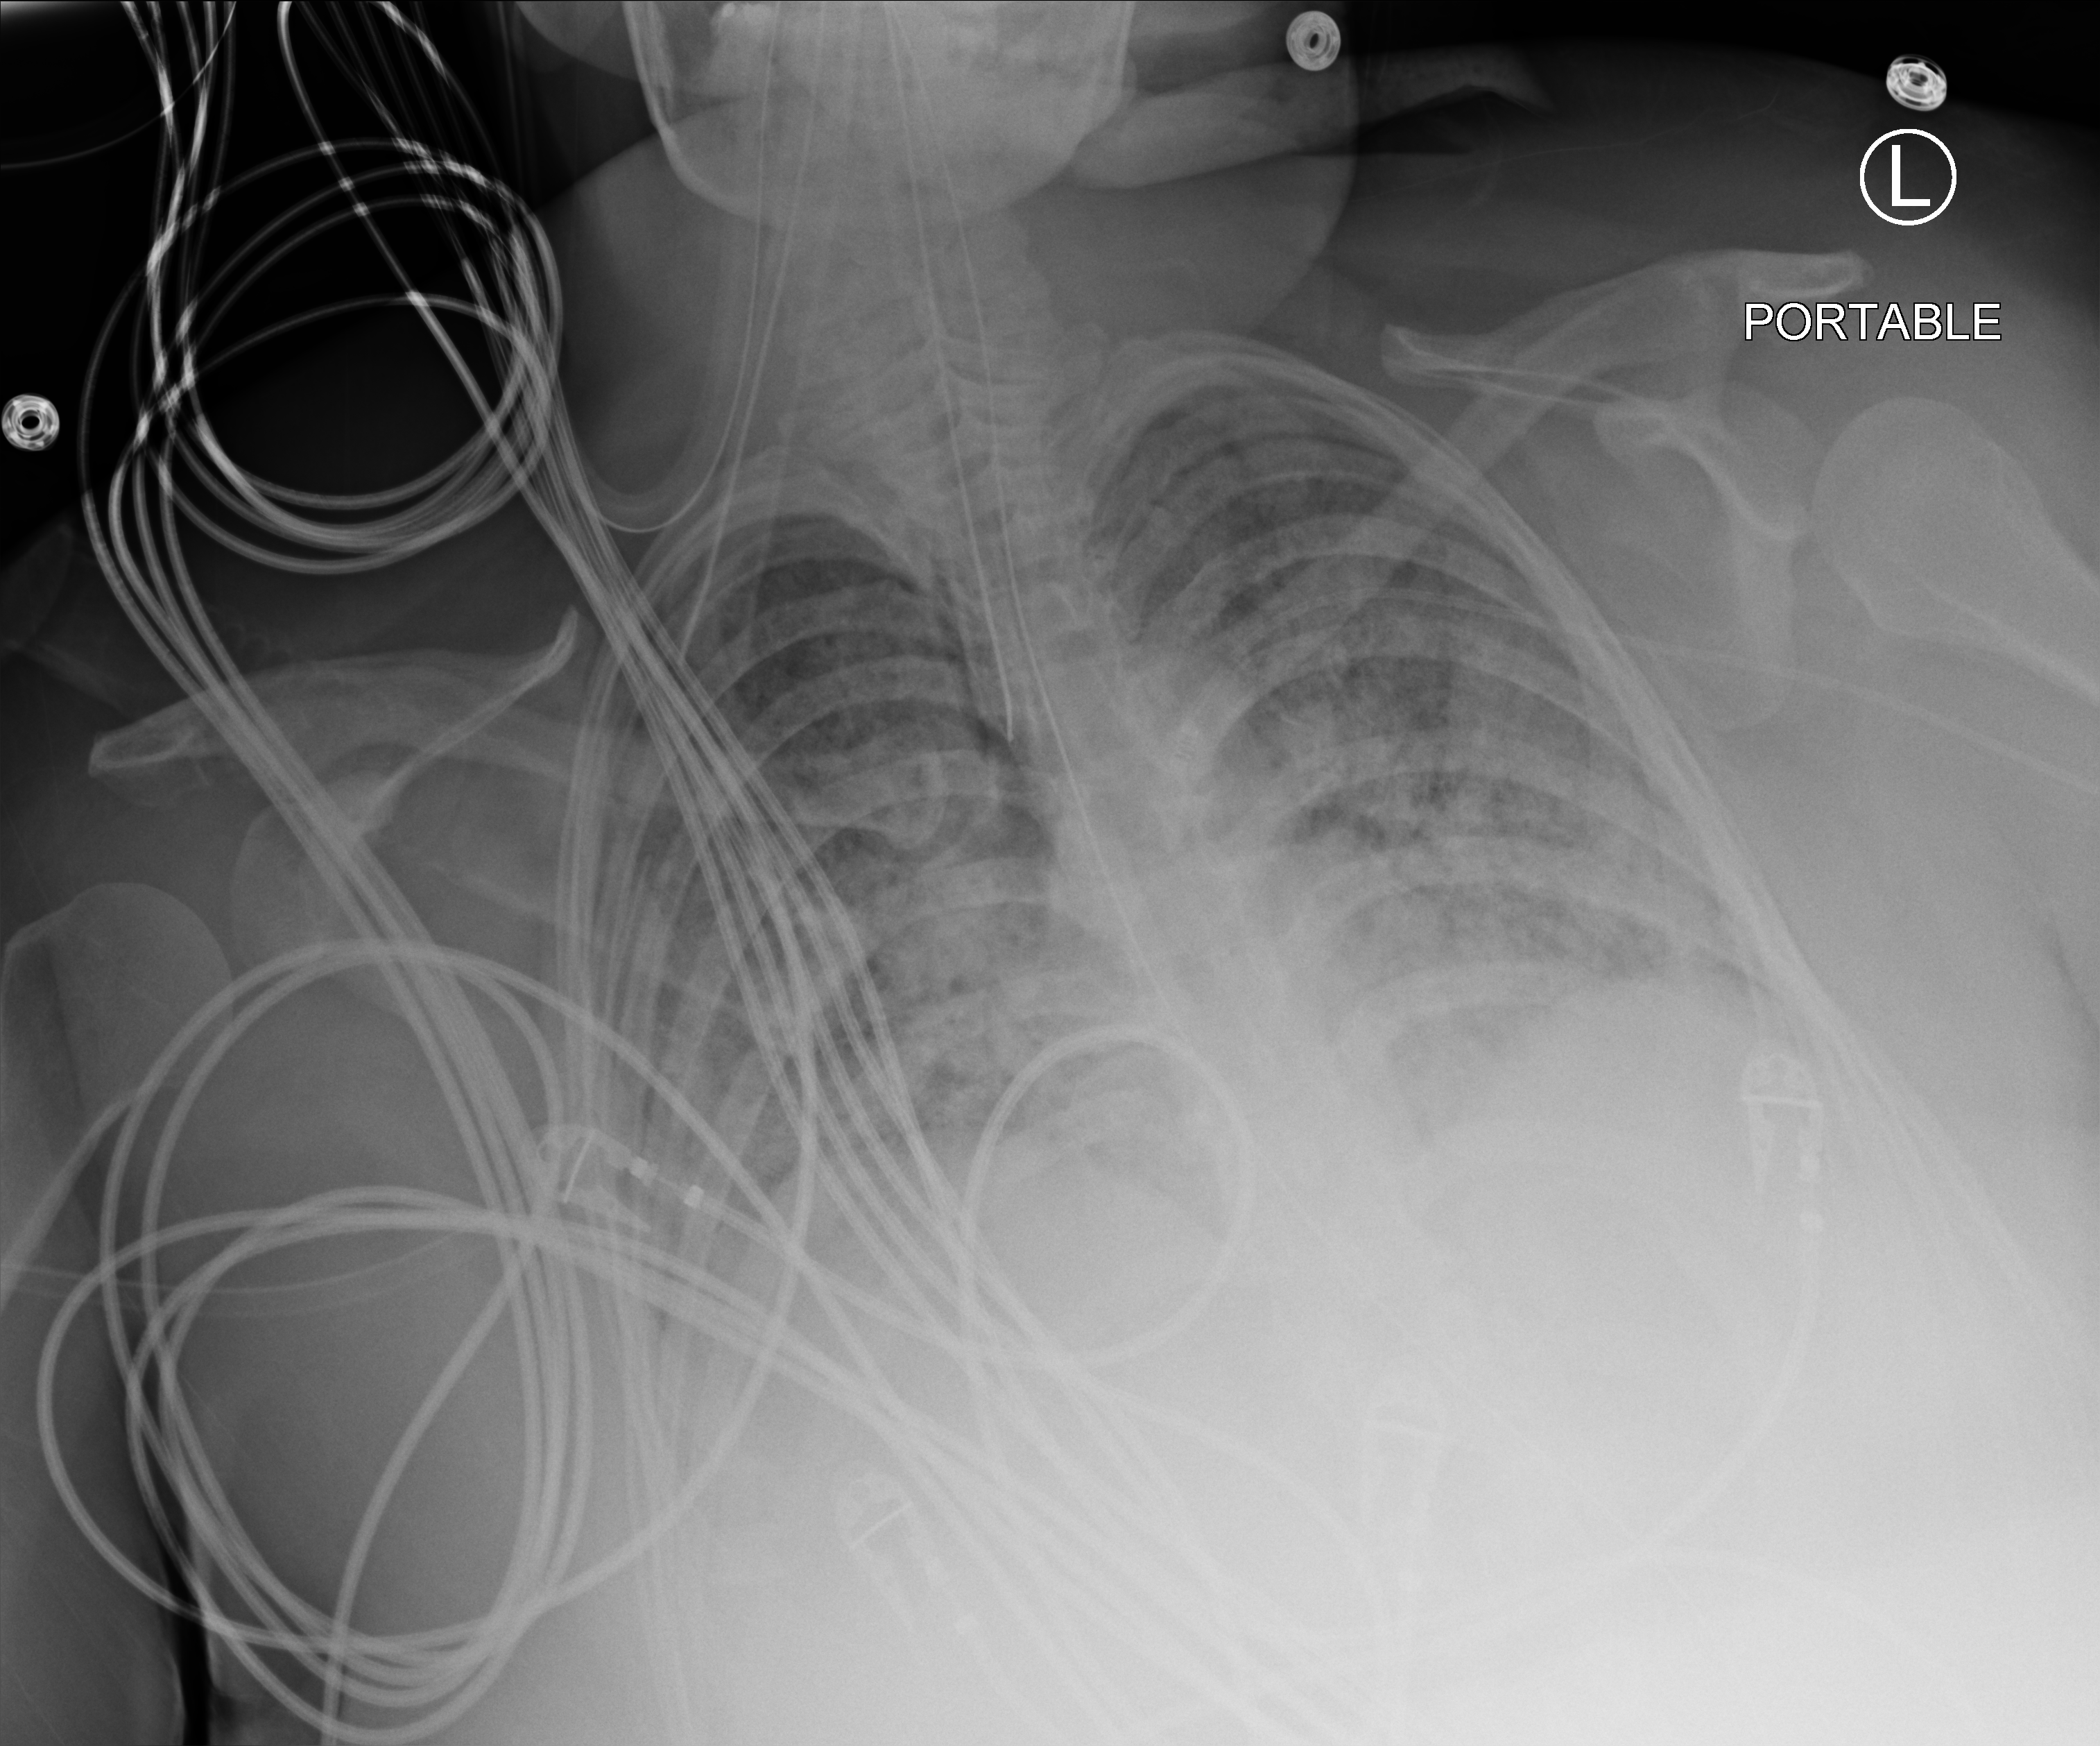
Chest X-ray (portable). Female patient hospitalised with COVID-19, age 18–59 years.
From the hospital-stay record, not from the radiograph (when in the stay this image was taken is not recorded): mechanically ventilated during this hospital stay: yes; smoking status (admission record): never.